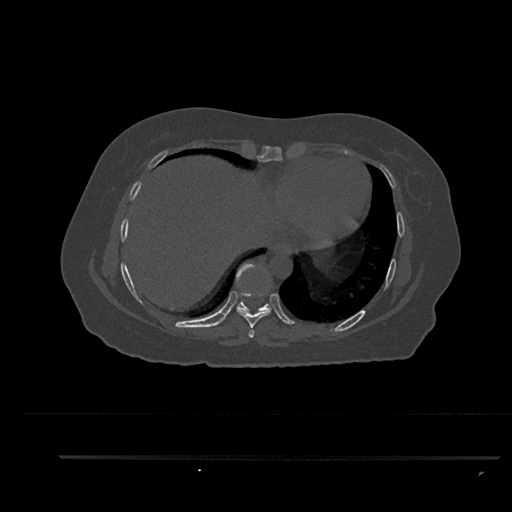
CT including the spine, one axial slice; slice 442 of 797 in the series (ordered by position); reconstruction kernel Br40s/3; 120 kVp; bone window (W 1800 / L 400 HU); 512 × 512 image matrix. Patient: female, 44 years. From the clinical record (not read from this slice): primary cancer: renal; vertebrae with lytic lesions (as recorded): L1.
Annotated regions visible in this slice (semi-automatic segmentation, software-assisted and operator-edited):
- T7 vertebra: bounding box <248,329,255,338> (left, top, right, bottom; pixels)
- T8 vertebra: <236,310,271,328>
- T9 vertebra: <235,263,272,312>